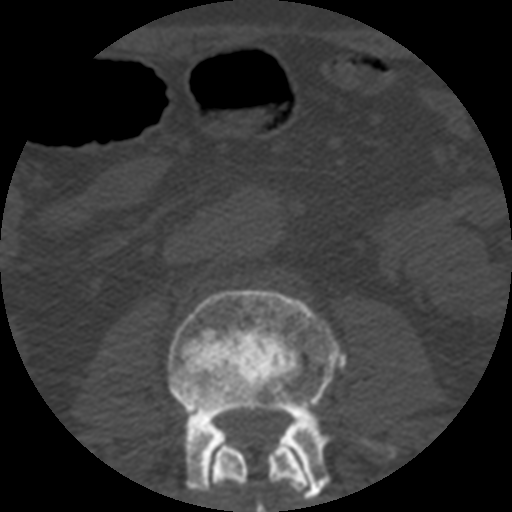
CT including the spine, one axial slice; slice 131 of 508 in the series (ordered by position); reconstruction kernel STANDARD; 120 kVp; bone window (W 1800 / L 400 HU); 1.25 mm slice thickness; 512 × 512 image matrix. Patient age 57 years. Case-level facts recorded for this patient, not image findings: primary cancer: prostate.
Structures marked on this image (semi-automatic segmentation, software-assisted and operator-edited):
- L2 vertebra: bounding box [x1, y1, x2, y2] px = [204, 434, 312, 512]
- L3 vertebra: [167, 289, 400, 501]